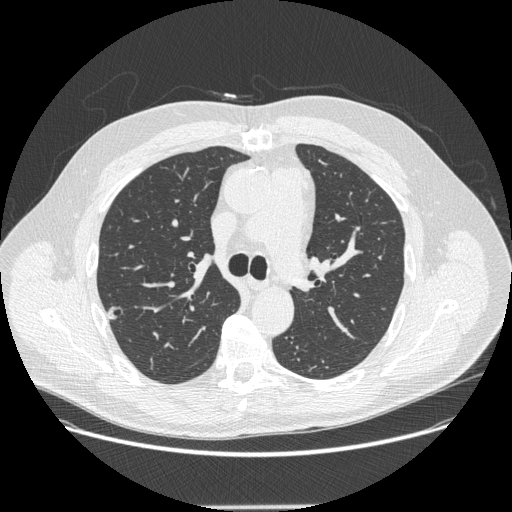
Low-dose screening chest CT, one axial slice. Slice 186 of 265 in the series (ordered by position). Reconstruction kernel STANDARD. 120 kVp. Lung window (W 1500 / L -600 HU). 1.25 mm slice thickness. 512 × 512 image matrix, field of view 400 × 400 mm.
Outlined on this slice (expert manual segmentation):
- lesion 1 (tumor, upper lobe of right lung): bounding box <108,306,123,319> (left, top, right, bottom; pixels)